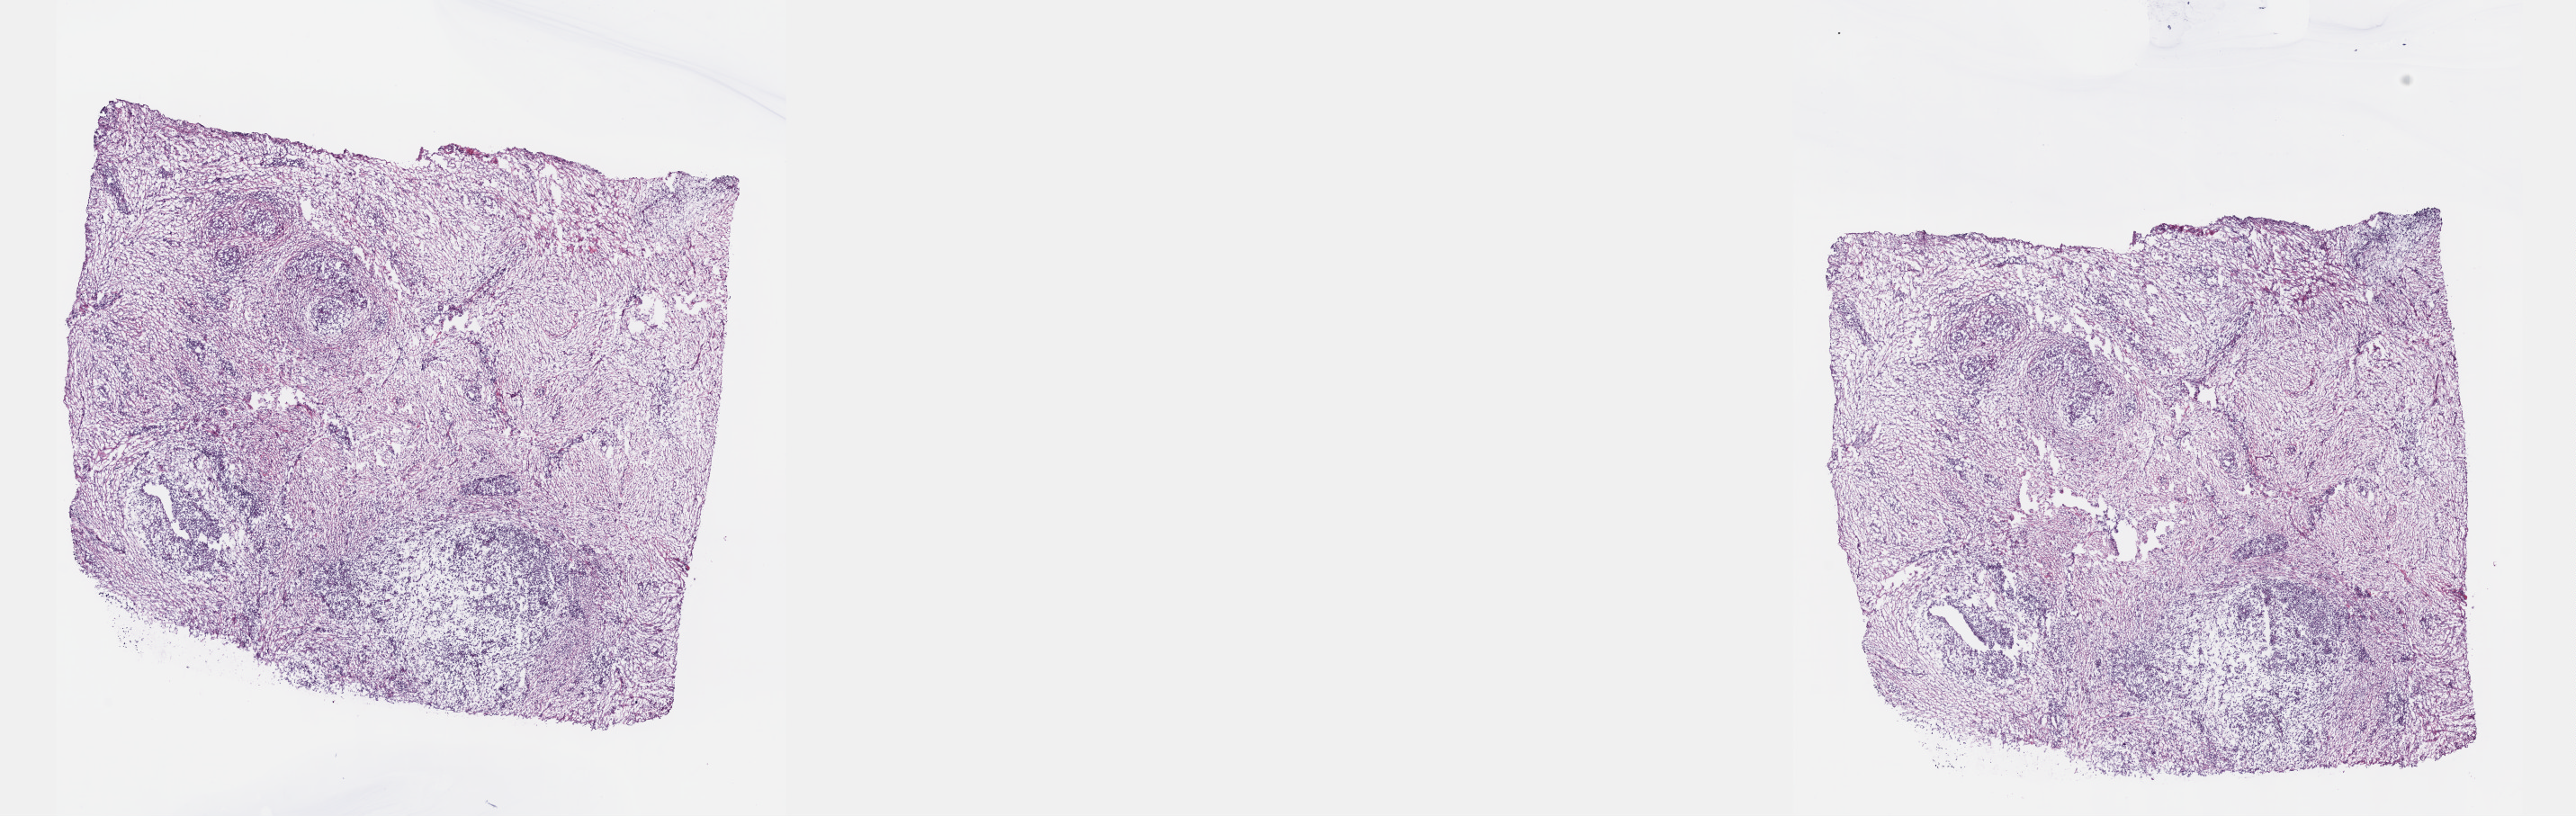
Digitized H&E-stained tissue section (whole slide), a low-resolution overview of the entire scanned area, about 23.1 x 7.3 mm (from a 40x scan). Frozen section from the top of the tissue portion. Sample: primary tumour, connective, subcutaneous and other soft tissues. Female patient; age at initial diagnosis 53 years. Composition of this section per pathologist review: tumour cells 100%, tumour nuclei 80%, normal cells 0%, stromal cells 0%, necrosis 0%. Inflammatory infiltration, as recorded: lymphocyte infiltration 1%, monocyte infiltration 0%, neutrophil infiltration 0%.
• diagnosis: Fibromyxosarcoma (connective, subcutaneous and other soft tissues of trunk, NOS)